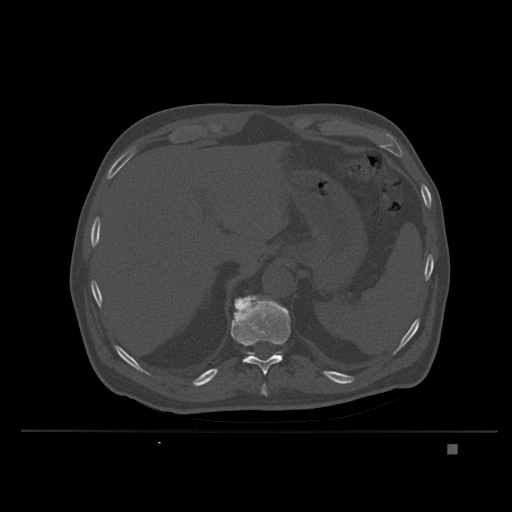
CT including the spine, one axial slice; position 175 of 435 along the scan axis; bone window (W 1800 / L 400 HU); 512 × 512 image matrix, field of view 434 × 434 mm. Patient: male, 73 years. Case-level facts recorded for this patient, not image findings: primary cancer: skin.
Annotated regions visible in this slice (semi-automatically segmented with operator editing):
- T10 vertebra: bounding box <261,384,268,396> (left, top, right, bottom; pixels)
- T11 vertebra: <230,296,291,375>
- T12 vertebra: <247,353,254,357>